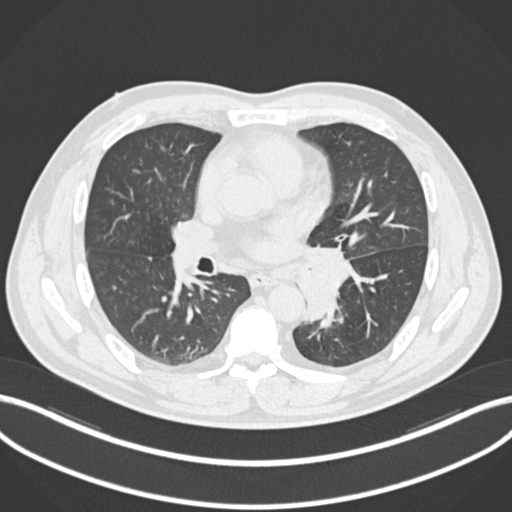
Chest CT, one axial slice; lung window (W 1500 / L -600 HU); 1 mm slice thickness; 512 × 512 image matrix, field of view 400 × 400 mm. Patient: male, 50 years. Case-level facts recorded for this patient, not image findings: clinical TNM (as recorded): T2a N3 M0.
Outlined on this slice (rectangle marked by the reading radiologist):
- lung tumour (recorded histology: squamous cell carcinoma): bounding box <297,244,354,324> (left, top, right, bottom; pixels)